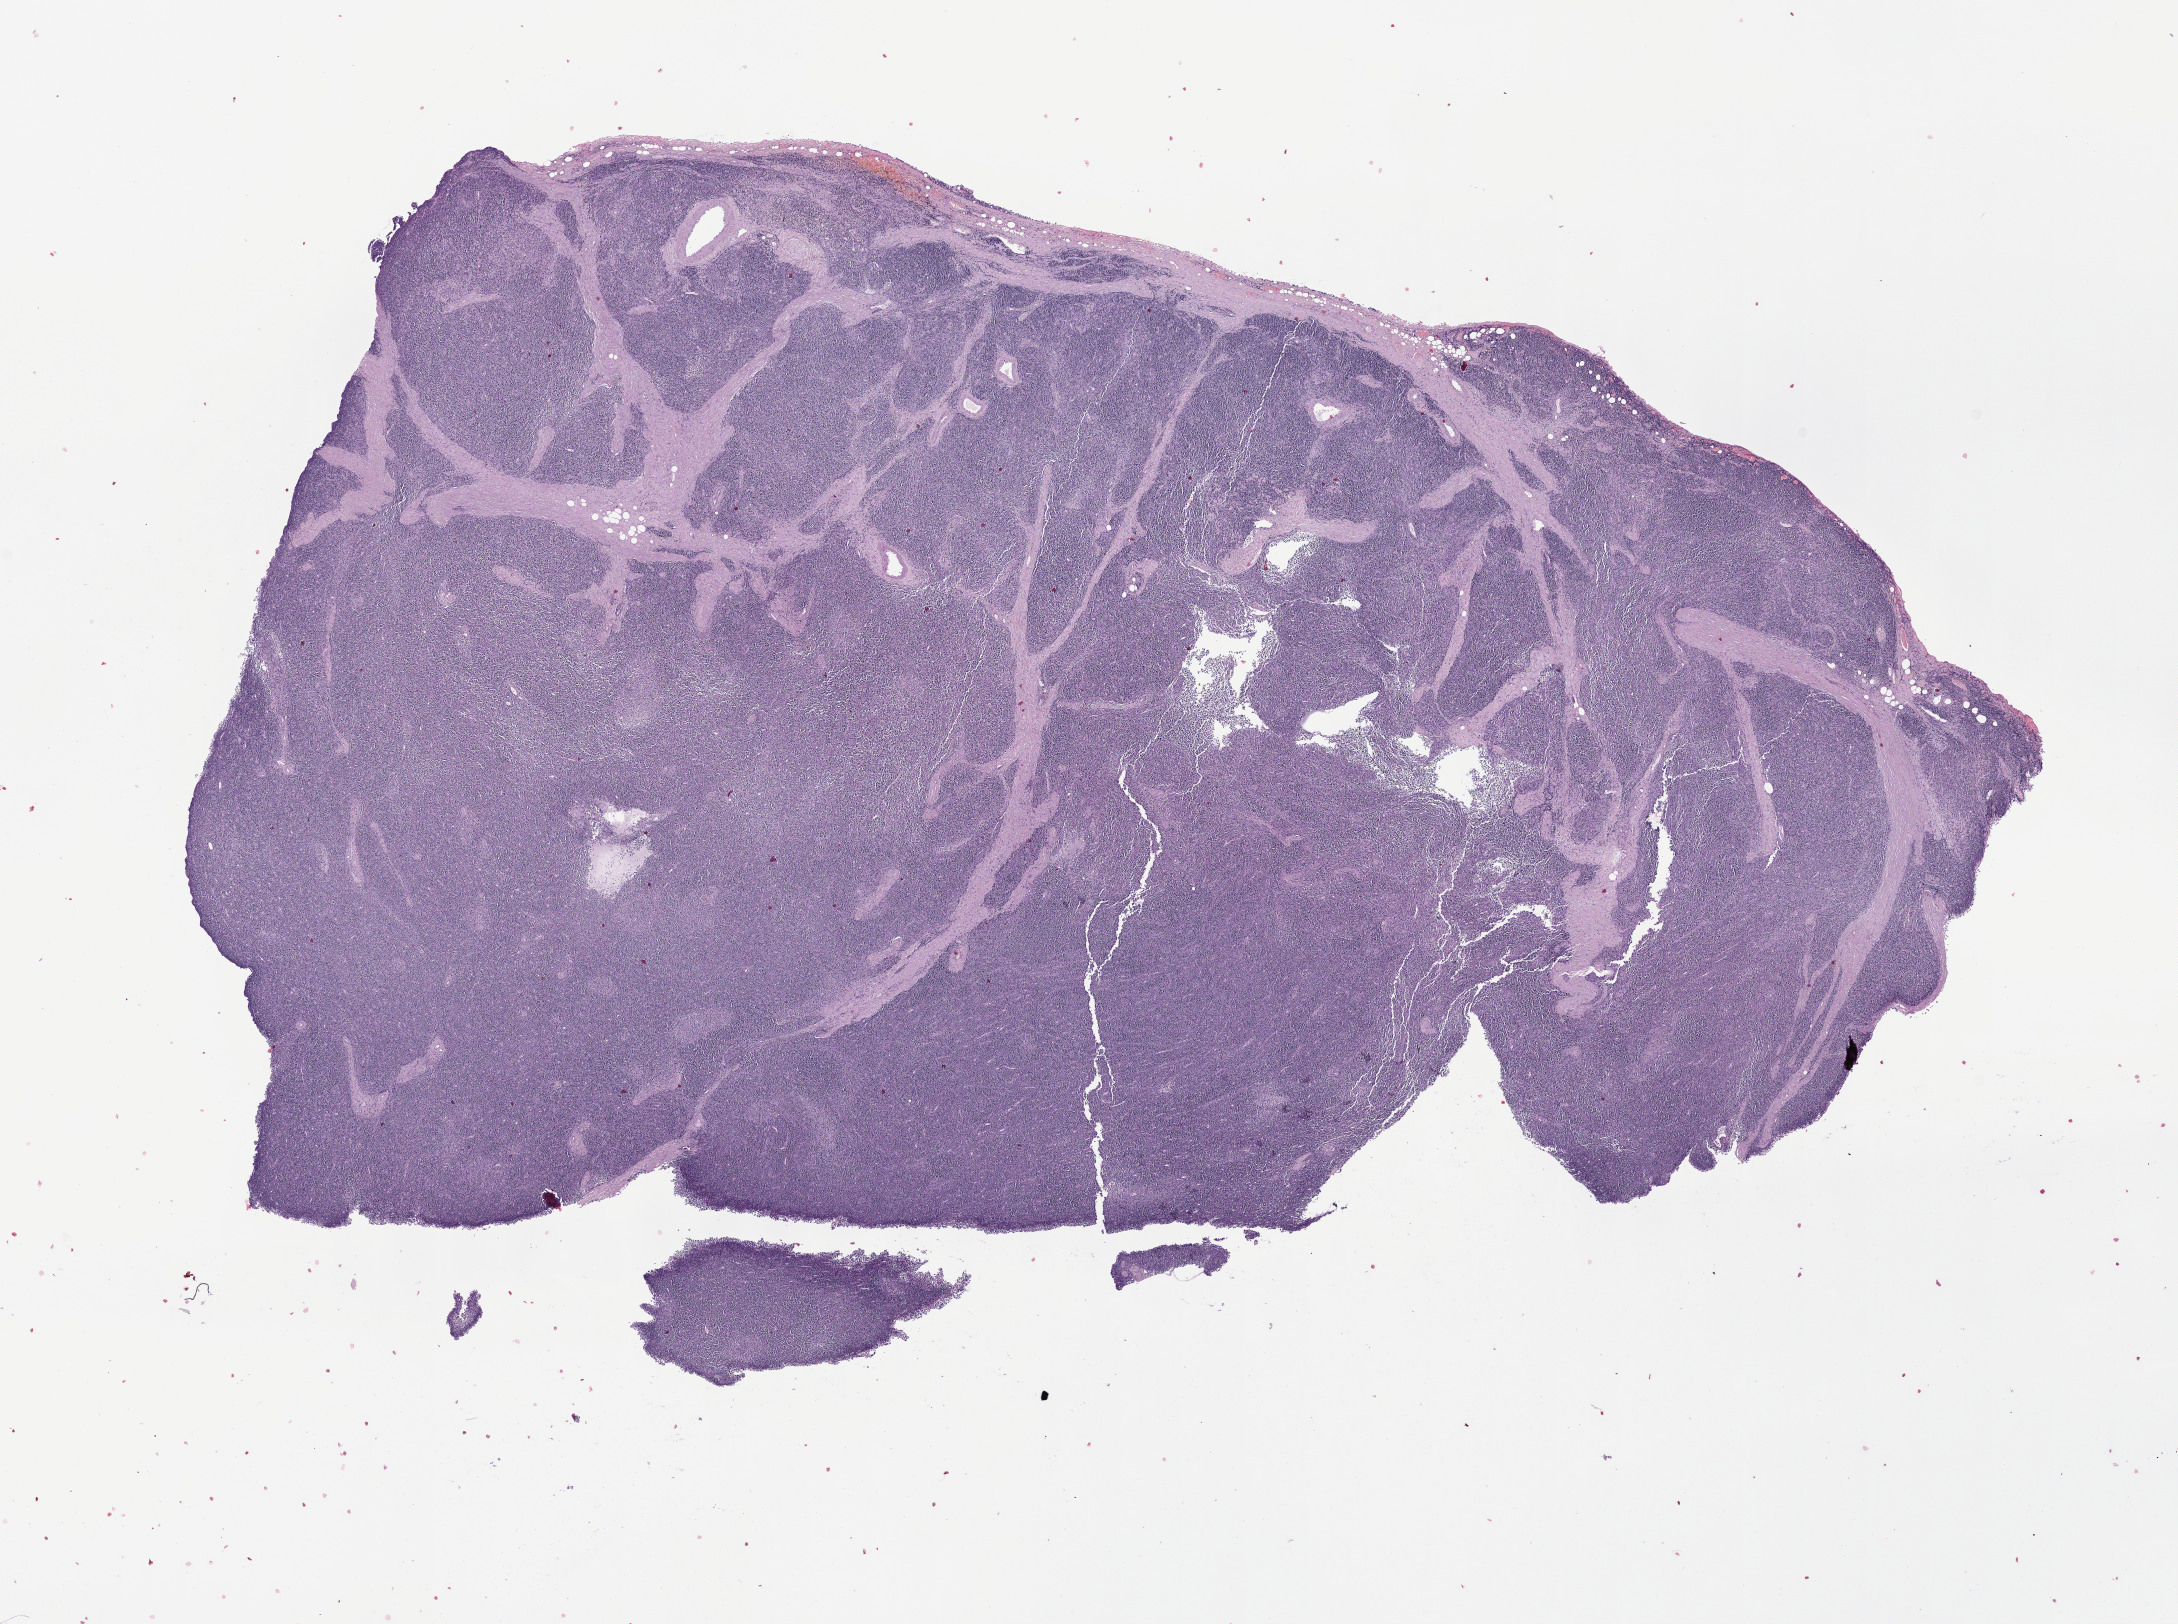
H&E-stained whole-slide image — a low-resolution overview of the entire scanned area, about 17.6 x 13.1 mm (slide scanned at 40x). Formalin-fixed paraffin-embedded (FFPE) diagnostic section. Sample: primary tumour, thymus. Male patient; age at initial diagnosis 52 years.
- histologic diagnosis: Thymoma, type B2, malignant (anterior mediastinum)